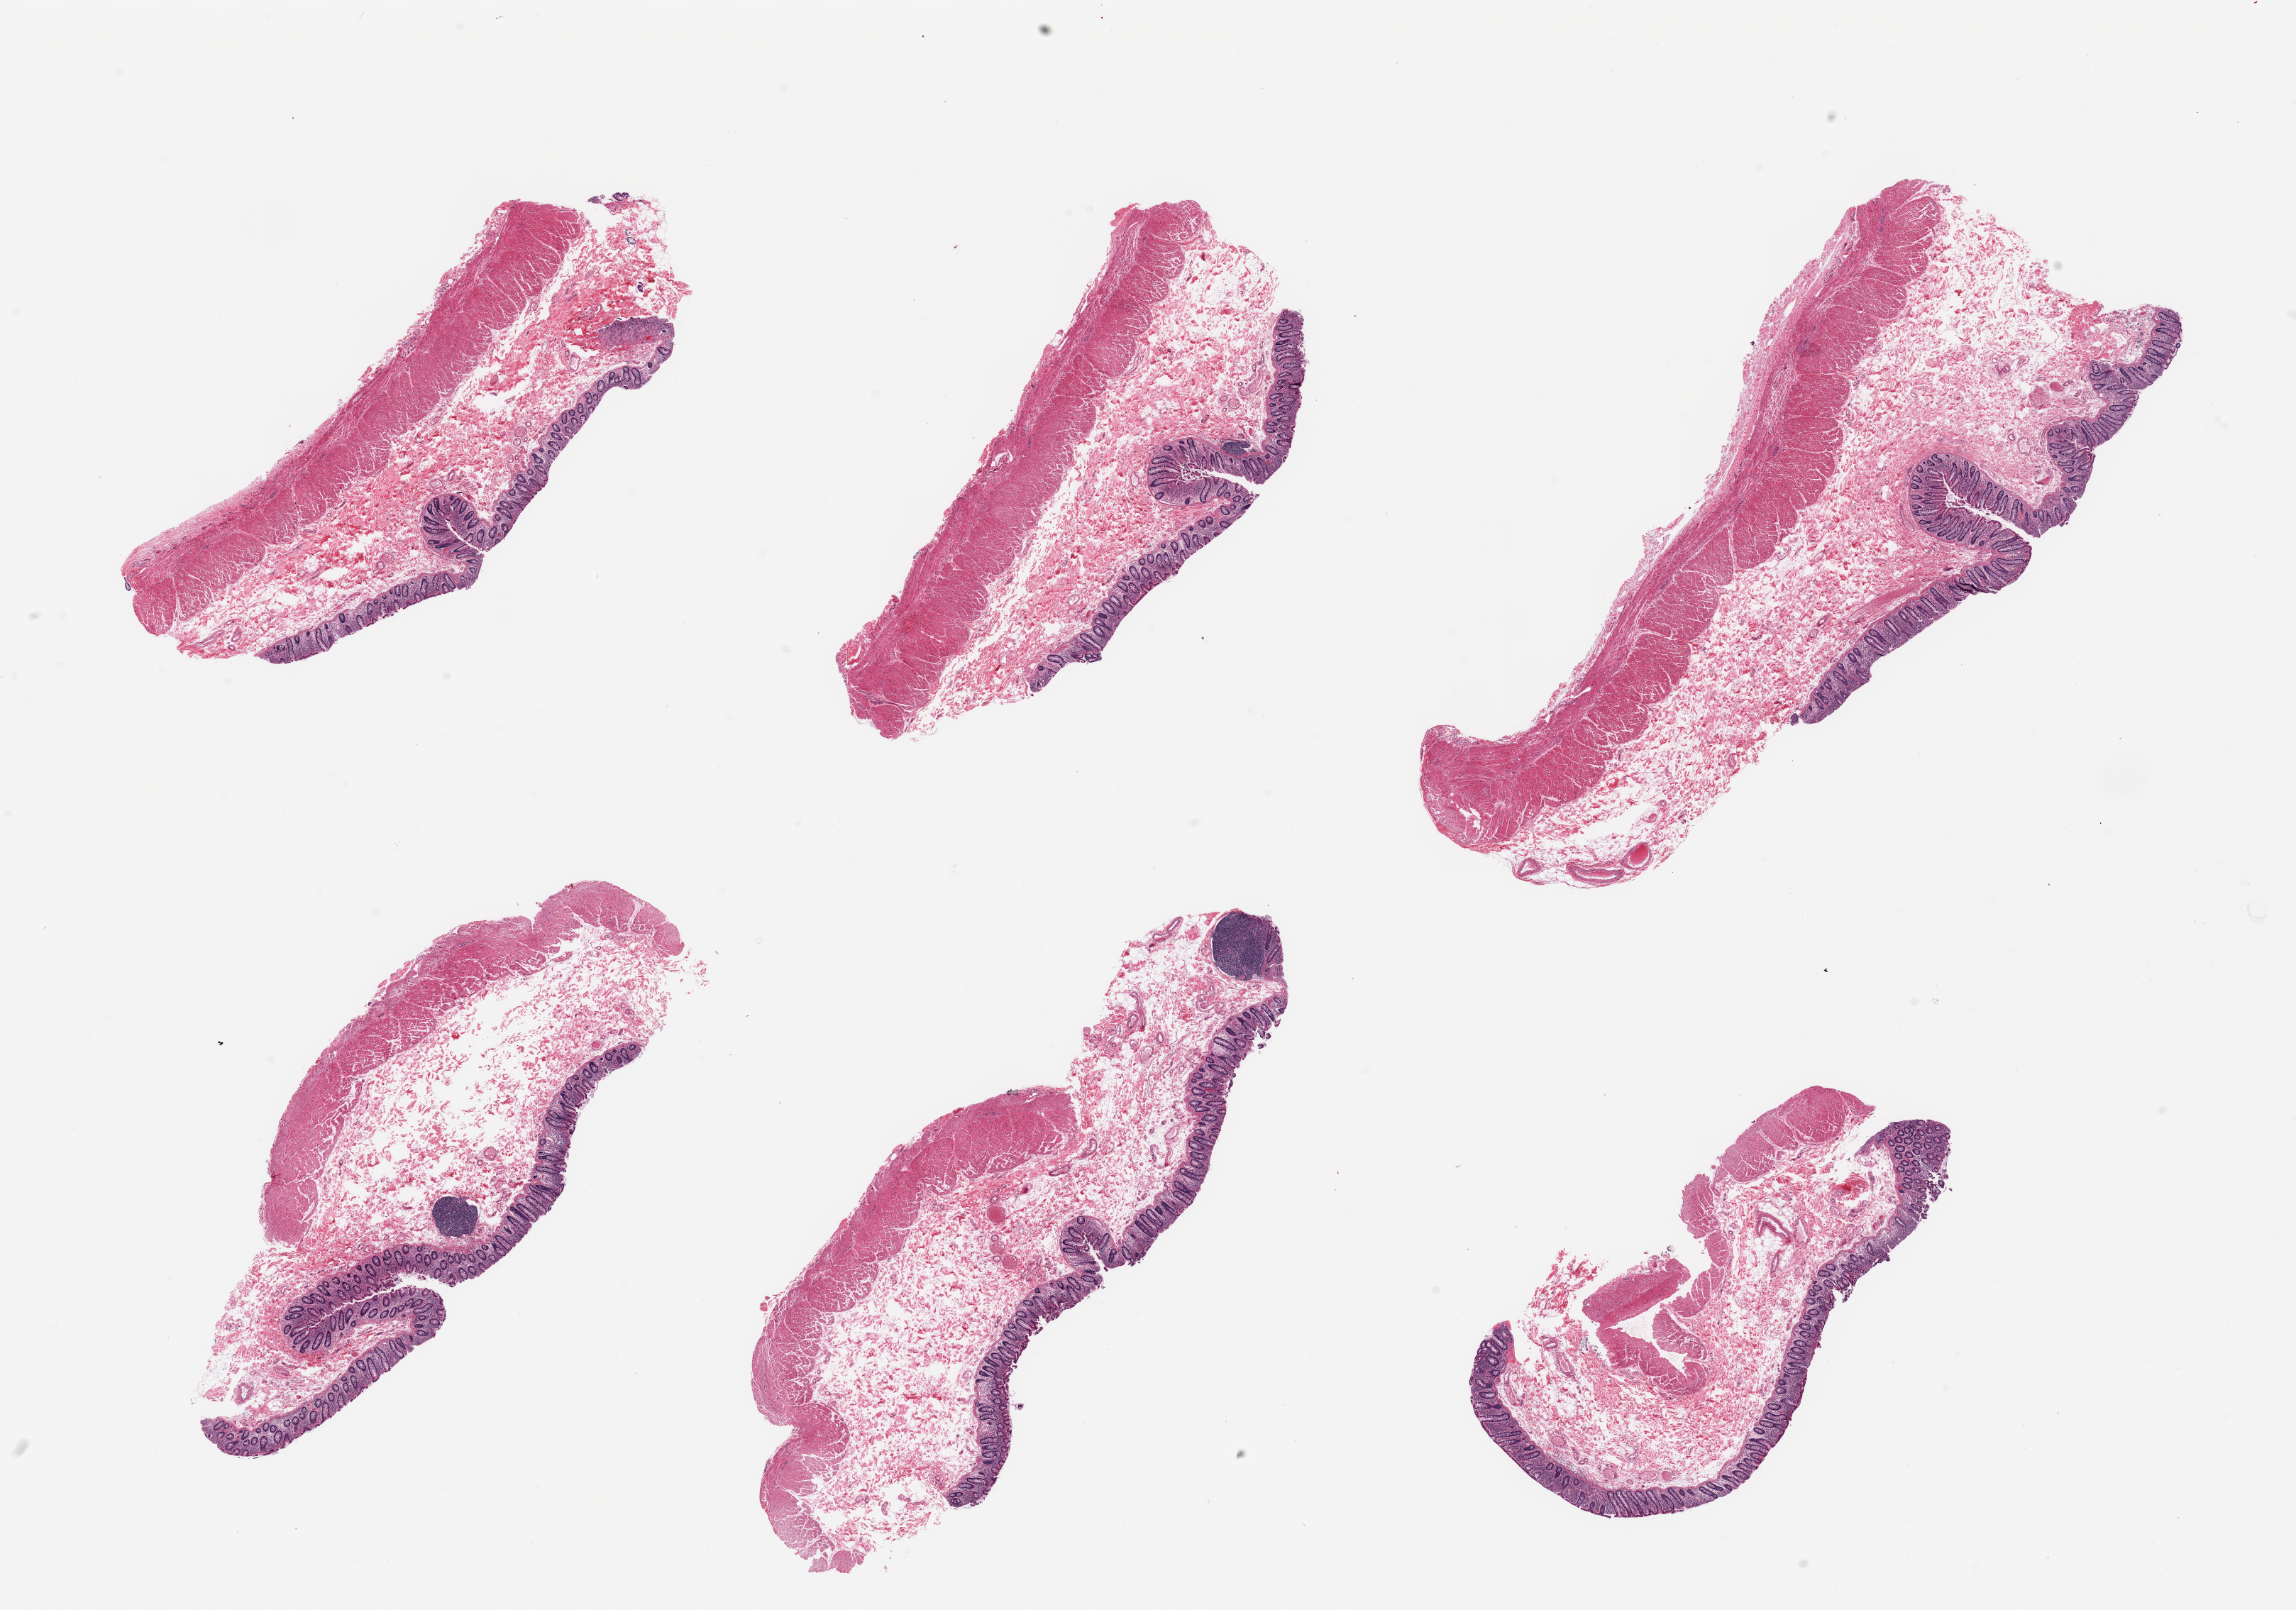
Digitized H&E-stained section — a low-resolution overview of the entire scanned area, about 25.6 x 17.9 mm (from a 20x scan). PAXgene-fixed, paraffin-embedded tissue. Sampled site (target tissue): transverse colon. Donor tissue sample. Female donor.
• pathologist's review note for this sample: 6 pieces, target mucosa well-preserved, up to ~0.35mm